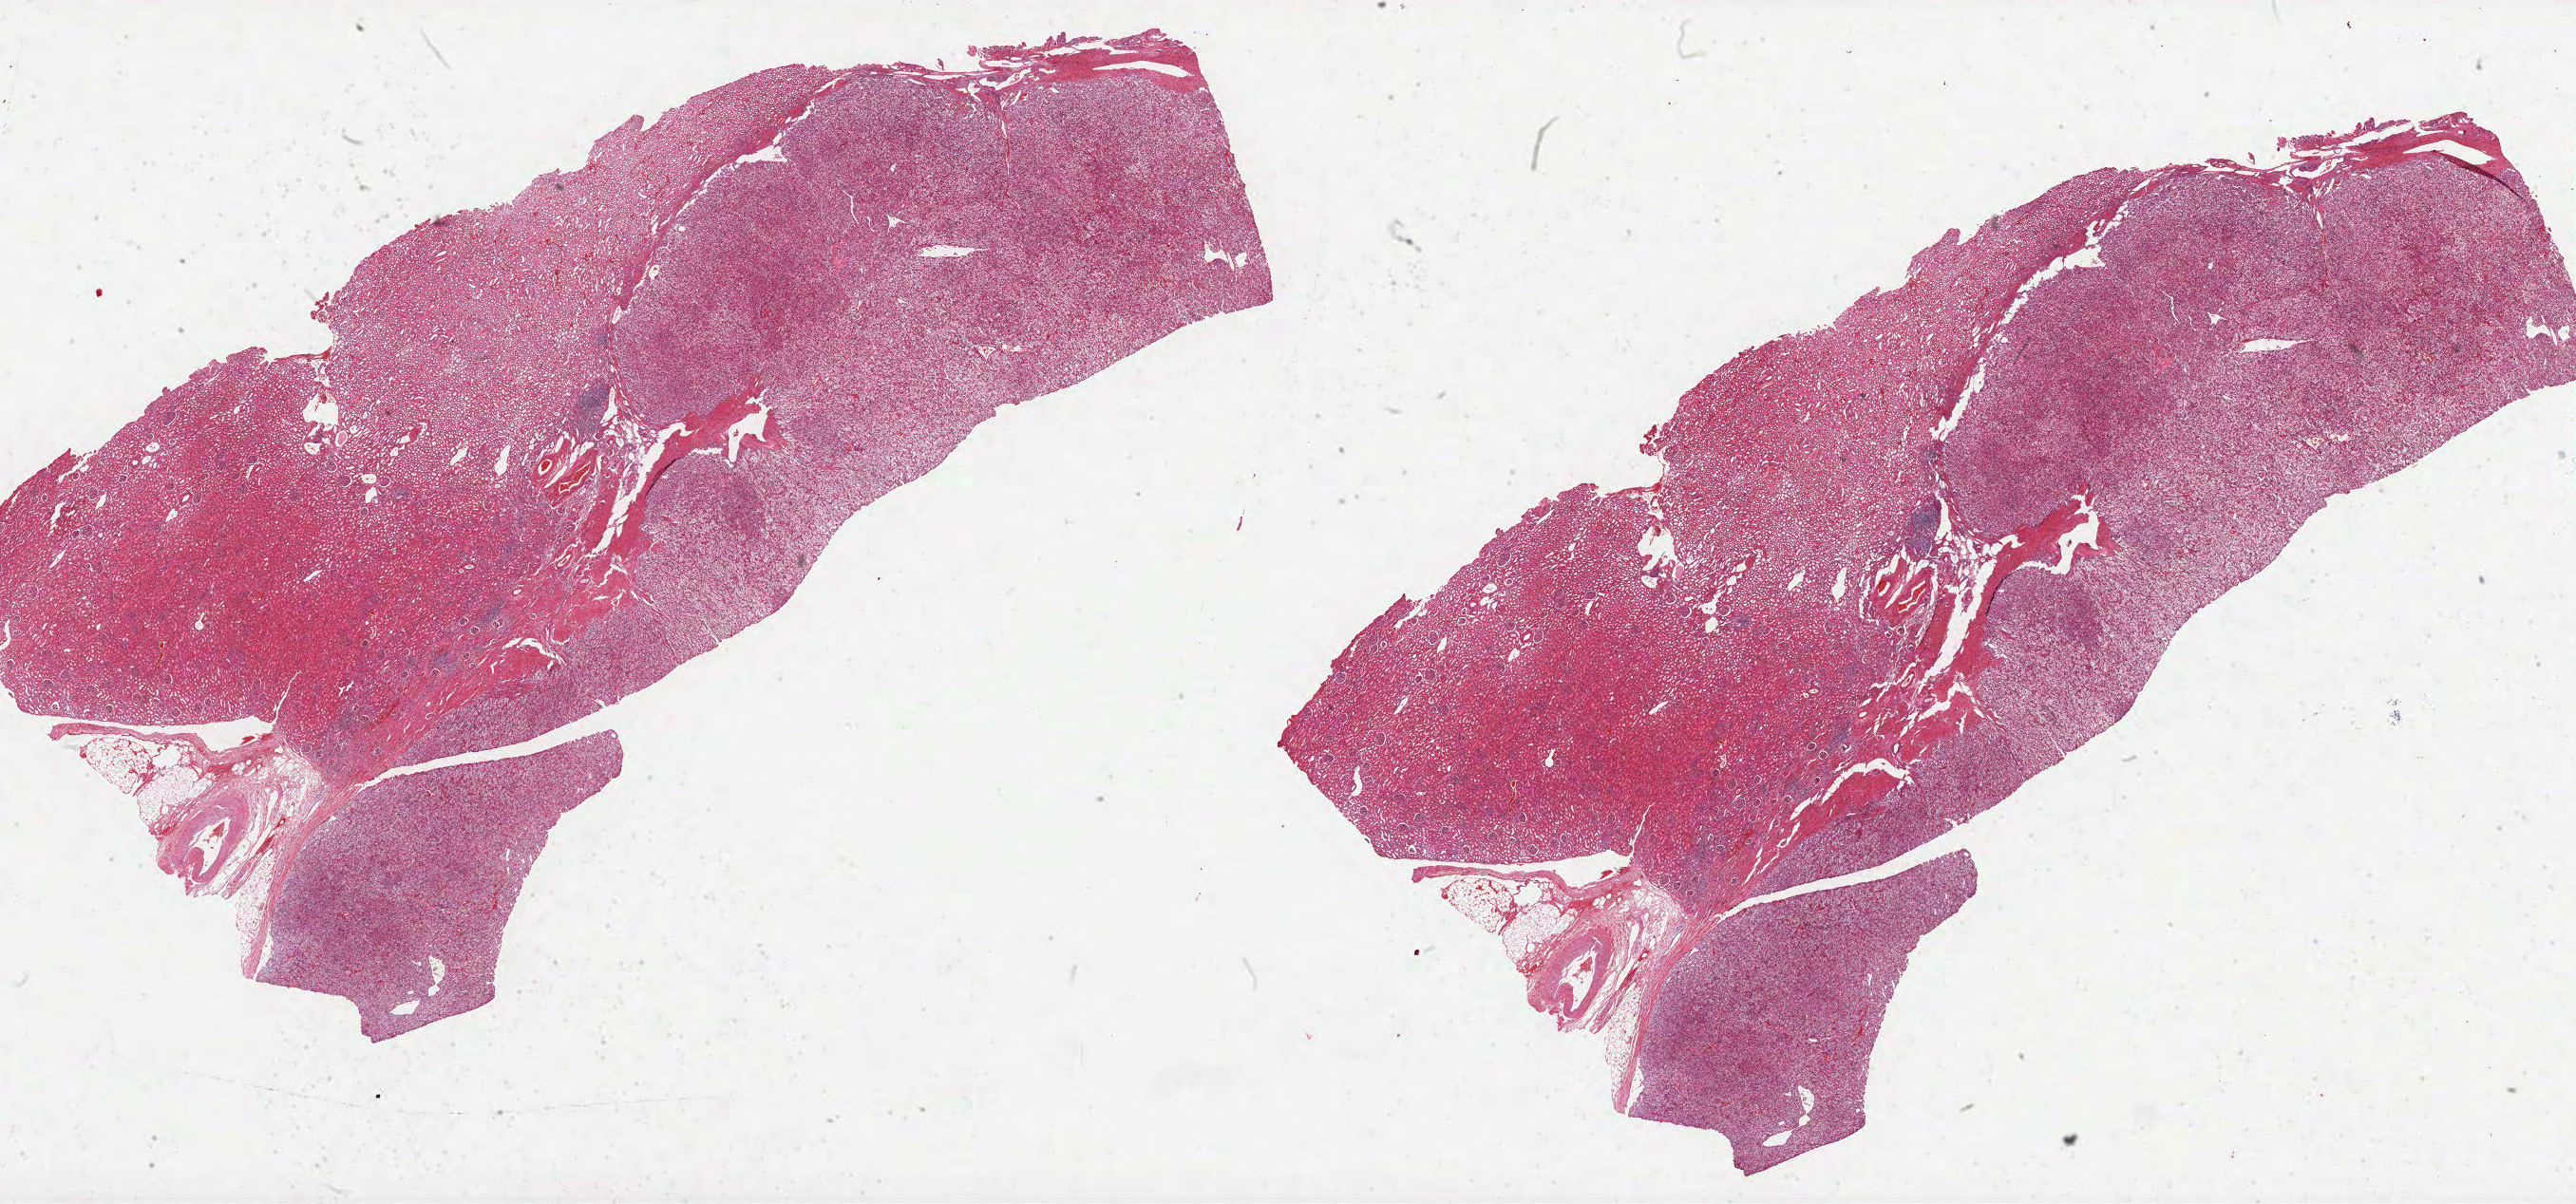
Whole-slide histology image, H&E — a low-resolution overview of the entire scanned area, about 43.8 x 20.5 mm. FFPE section. Sample: primary tumour, kidney. Male patient; age at initial diagnosis 77 years. Histologic grade: G3 (poorly differentiated).
• TNM: T1b N0 M0
• laterality: right
• histologic diagnosis: Clear cell adenocarcinoma, NOS
• AJCC pathologic stage: I